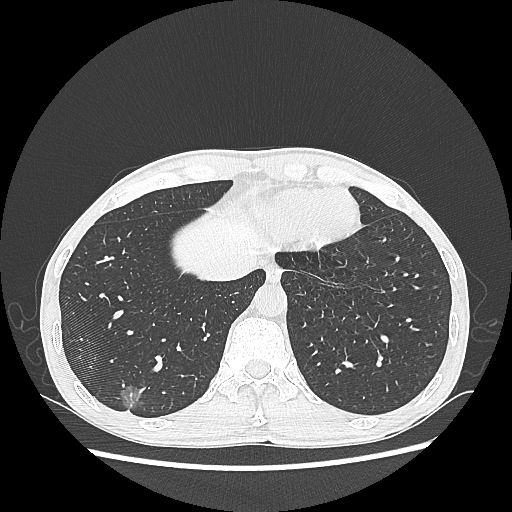
Chest CT, one axial slice; slice 67 of 270 in the series (ordered by position); reconstruction kernel LUNG; 100 kVp; lung window (W 1500 / L -600 HU); 512 × 512 image matrix, field of view 360 × 360 mm. Patient: male, 60 years. Case-level facts recorded for this patient, not image findings: clinical TNM (as recorded): T1c N0 M0; histopathological grade: G2.
Outlined on this slice (bounding box drawn by a radiologist):
- lung tumour (recorded histology: adenocarcinoma): bounding box [x1, y1, x2, y2] px = [117, 379, 142, 412]